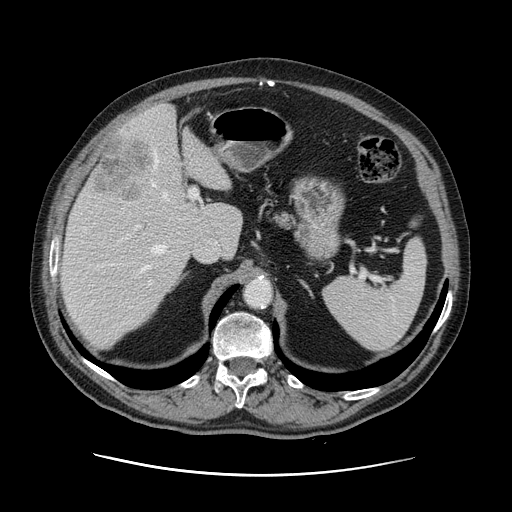
Contrast-enhanced abdominal CT, one axial slice. Slice 84 of 141 in the series (ordered by position). 120 kVp. Intravenous contrast given. Soft-tissue window (W 400 / L 40 HU). 2.5 mm slice thickness. 512 × 512 image matrix, field of view 395 × 395 mm. Male patient, age 72 years. Case-level facts recorded for this patient, not image findings: diagnosis: colorectal cancer liver metastases, imaged before liver resection; multiple liver metastases: yes; largest metastasis: 5.4 cm; chemotherapy before resection: yes.
Outlined on this slice (expert manual segmentation):
- hepatic veins: bounding box [x1, y1, x2, y2] px = [140, 150, 168, 272]
- liver: [61, 105, 242, 347]
- planned liver remnant (the part of the liver to remain after resection): [61, 129, 243, 347]
- portal vein (with intrahepatic branches): [128, 188, 198, 282]
- liver metastasis: [95, 140, 152, 201]